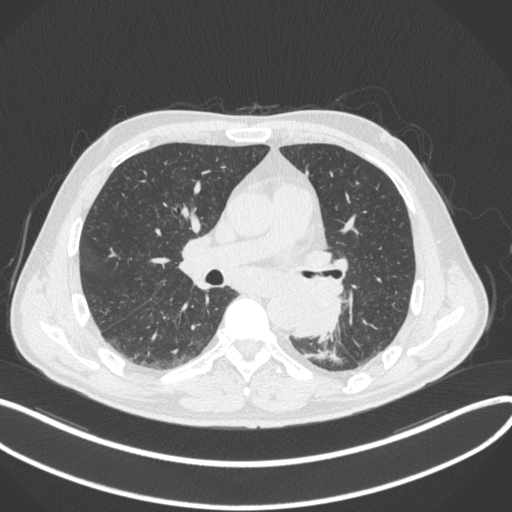
Chest CT, one axial slice. Reconstruction kernel B31f. 120 kVp. Lung window (W 1500 / L -600 HU). 1 mm slice thickness. 512 × 512 image matrix, field of view 400 × 400 mm. Male patient, age 59 years. Case-level facts recorded for this patient, not image findings: clinical TNM (as recorded): T2a N2 M0.
Annotated regions visible in this slice (rectangle marked by the reading radiologist):
- lung tumour (recorded histology: squamous cell carcinoma): bounding box [x1, y1, x2, y2] px = [296, 285, 349, 344]